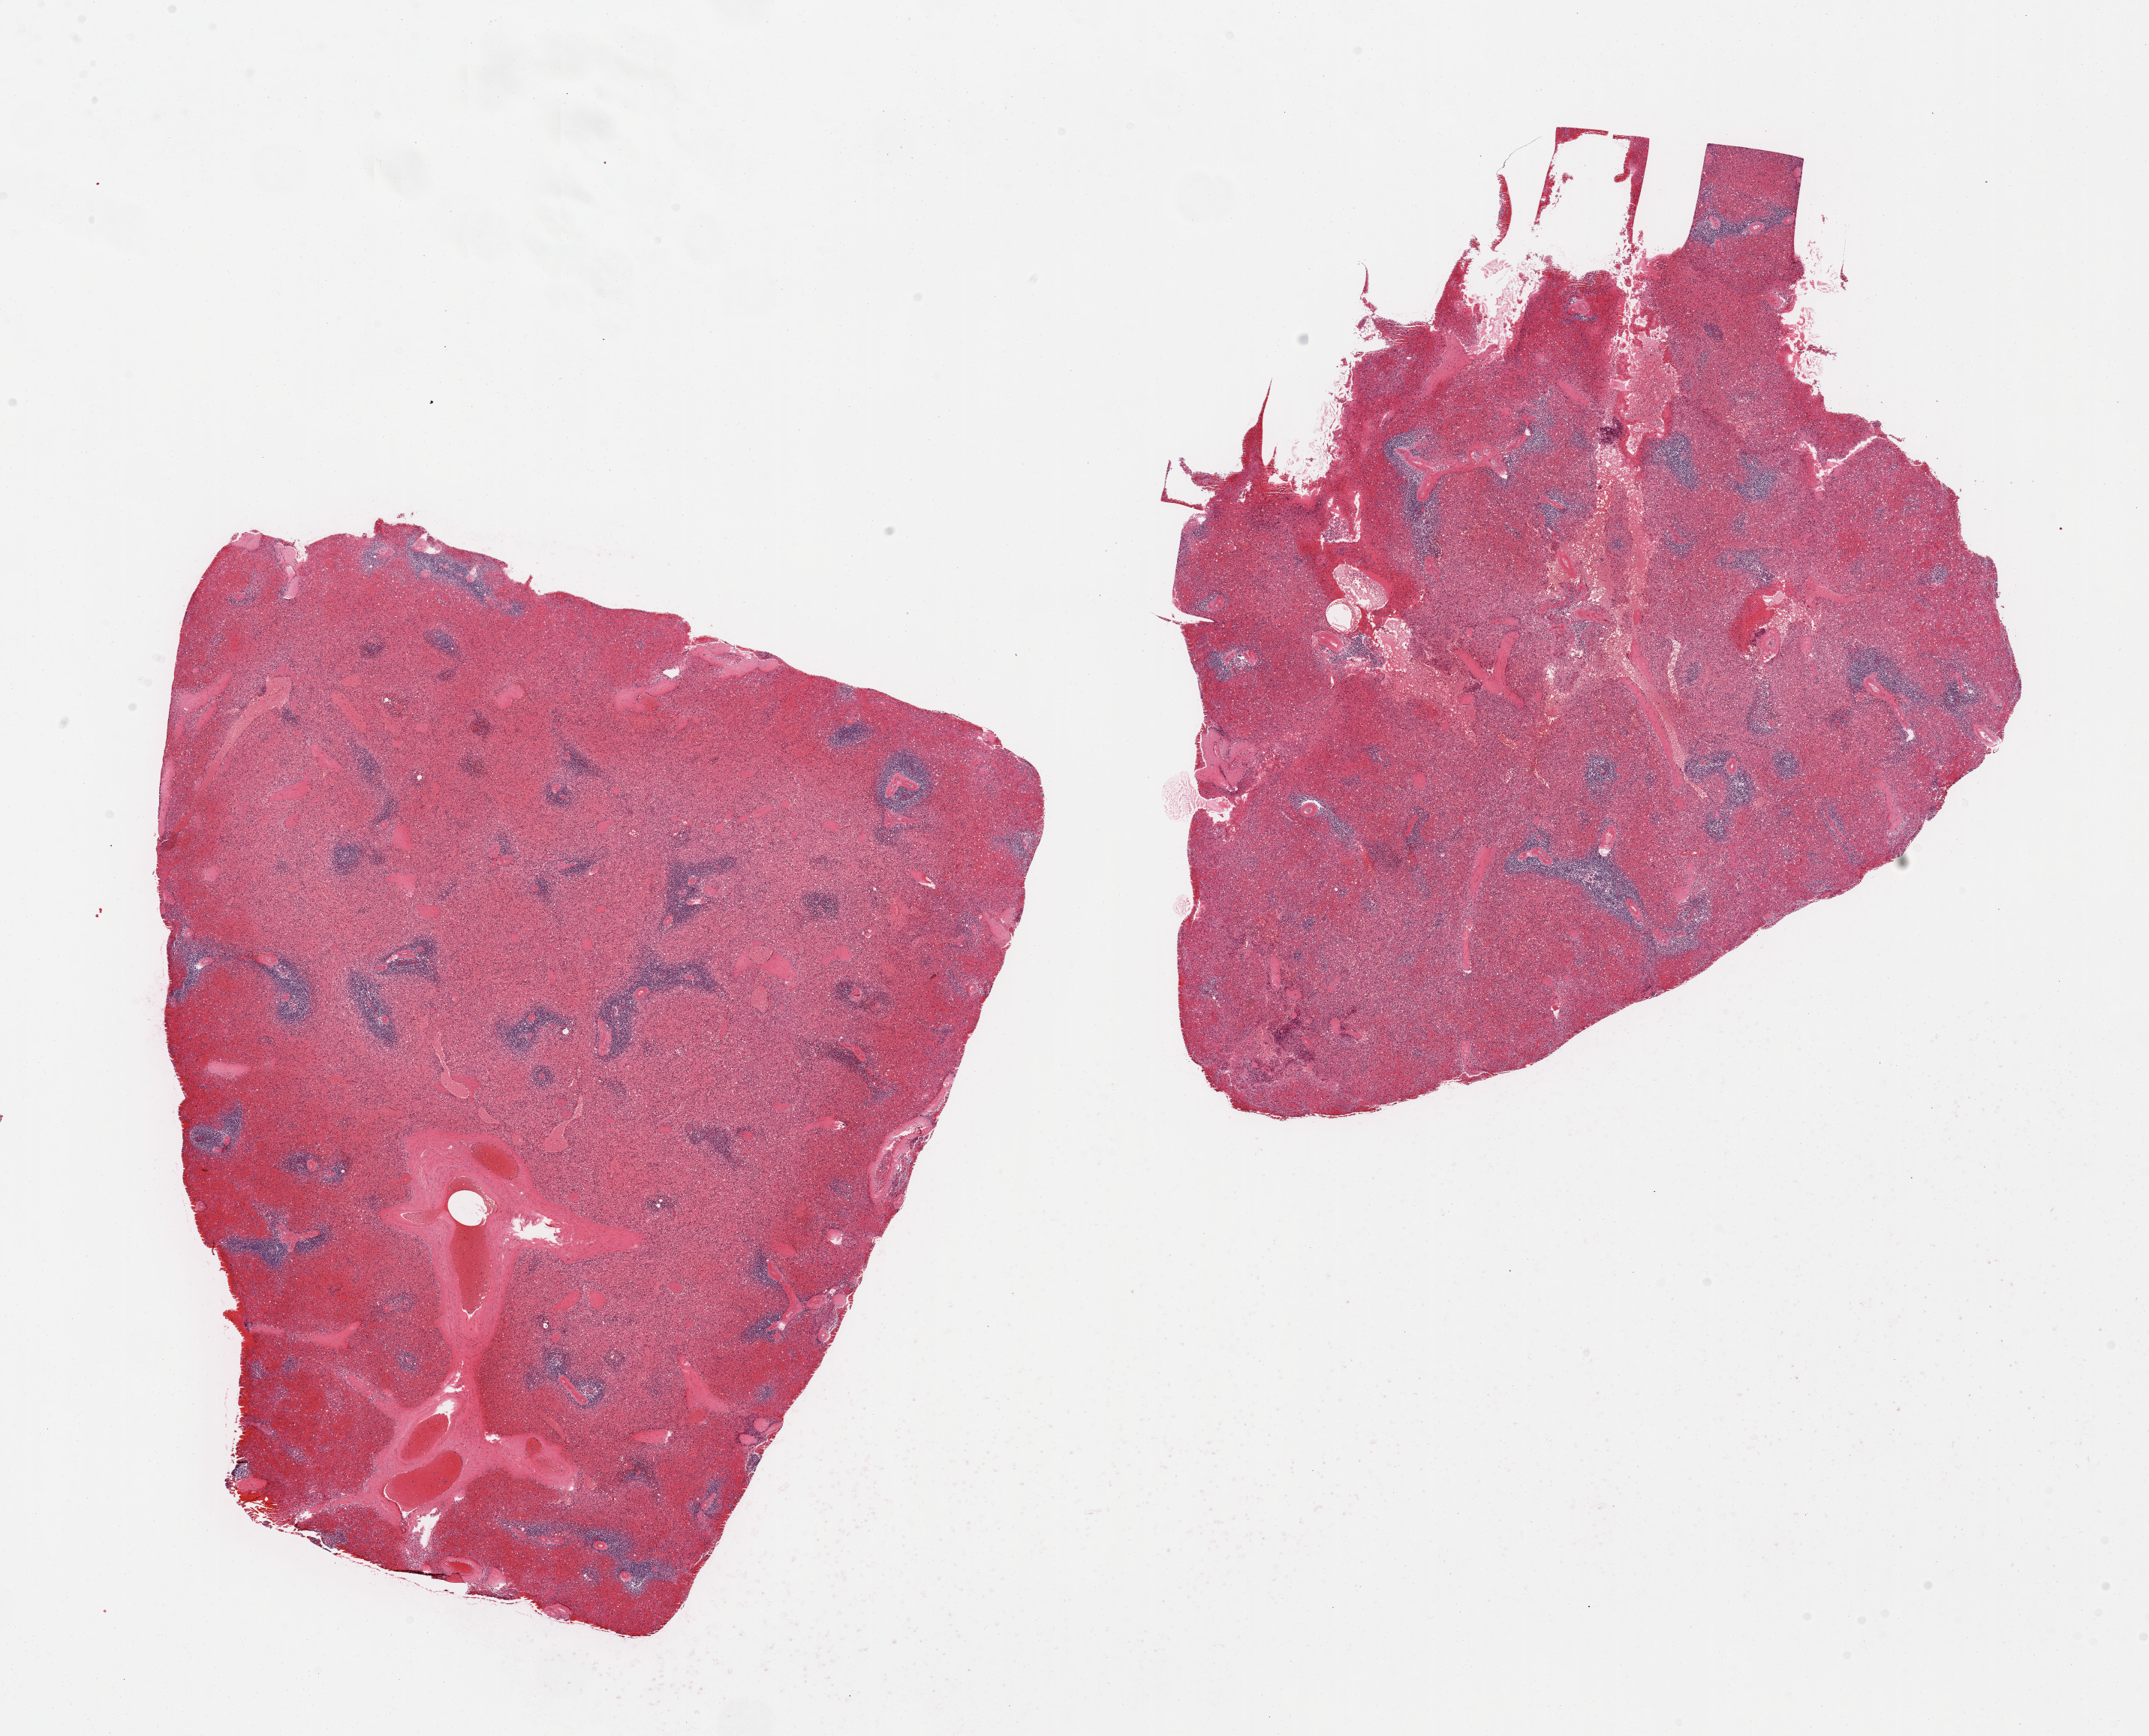
Whole-slide image, hematoxylin and eosin (H&E) stain, low-resolution overview of the scanned area, about 22.6 x 18.3 mm (slide scanned at 20x); PAXgene-fixed paraffin-embedded (PFPE) section; target tissue: spleen; tissue donor sample. Male donor.
Pathologist's review note for this sample: 2 pieces, moderate congestion.